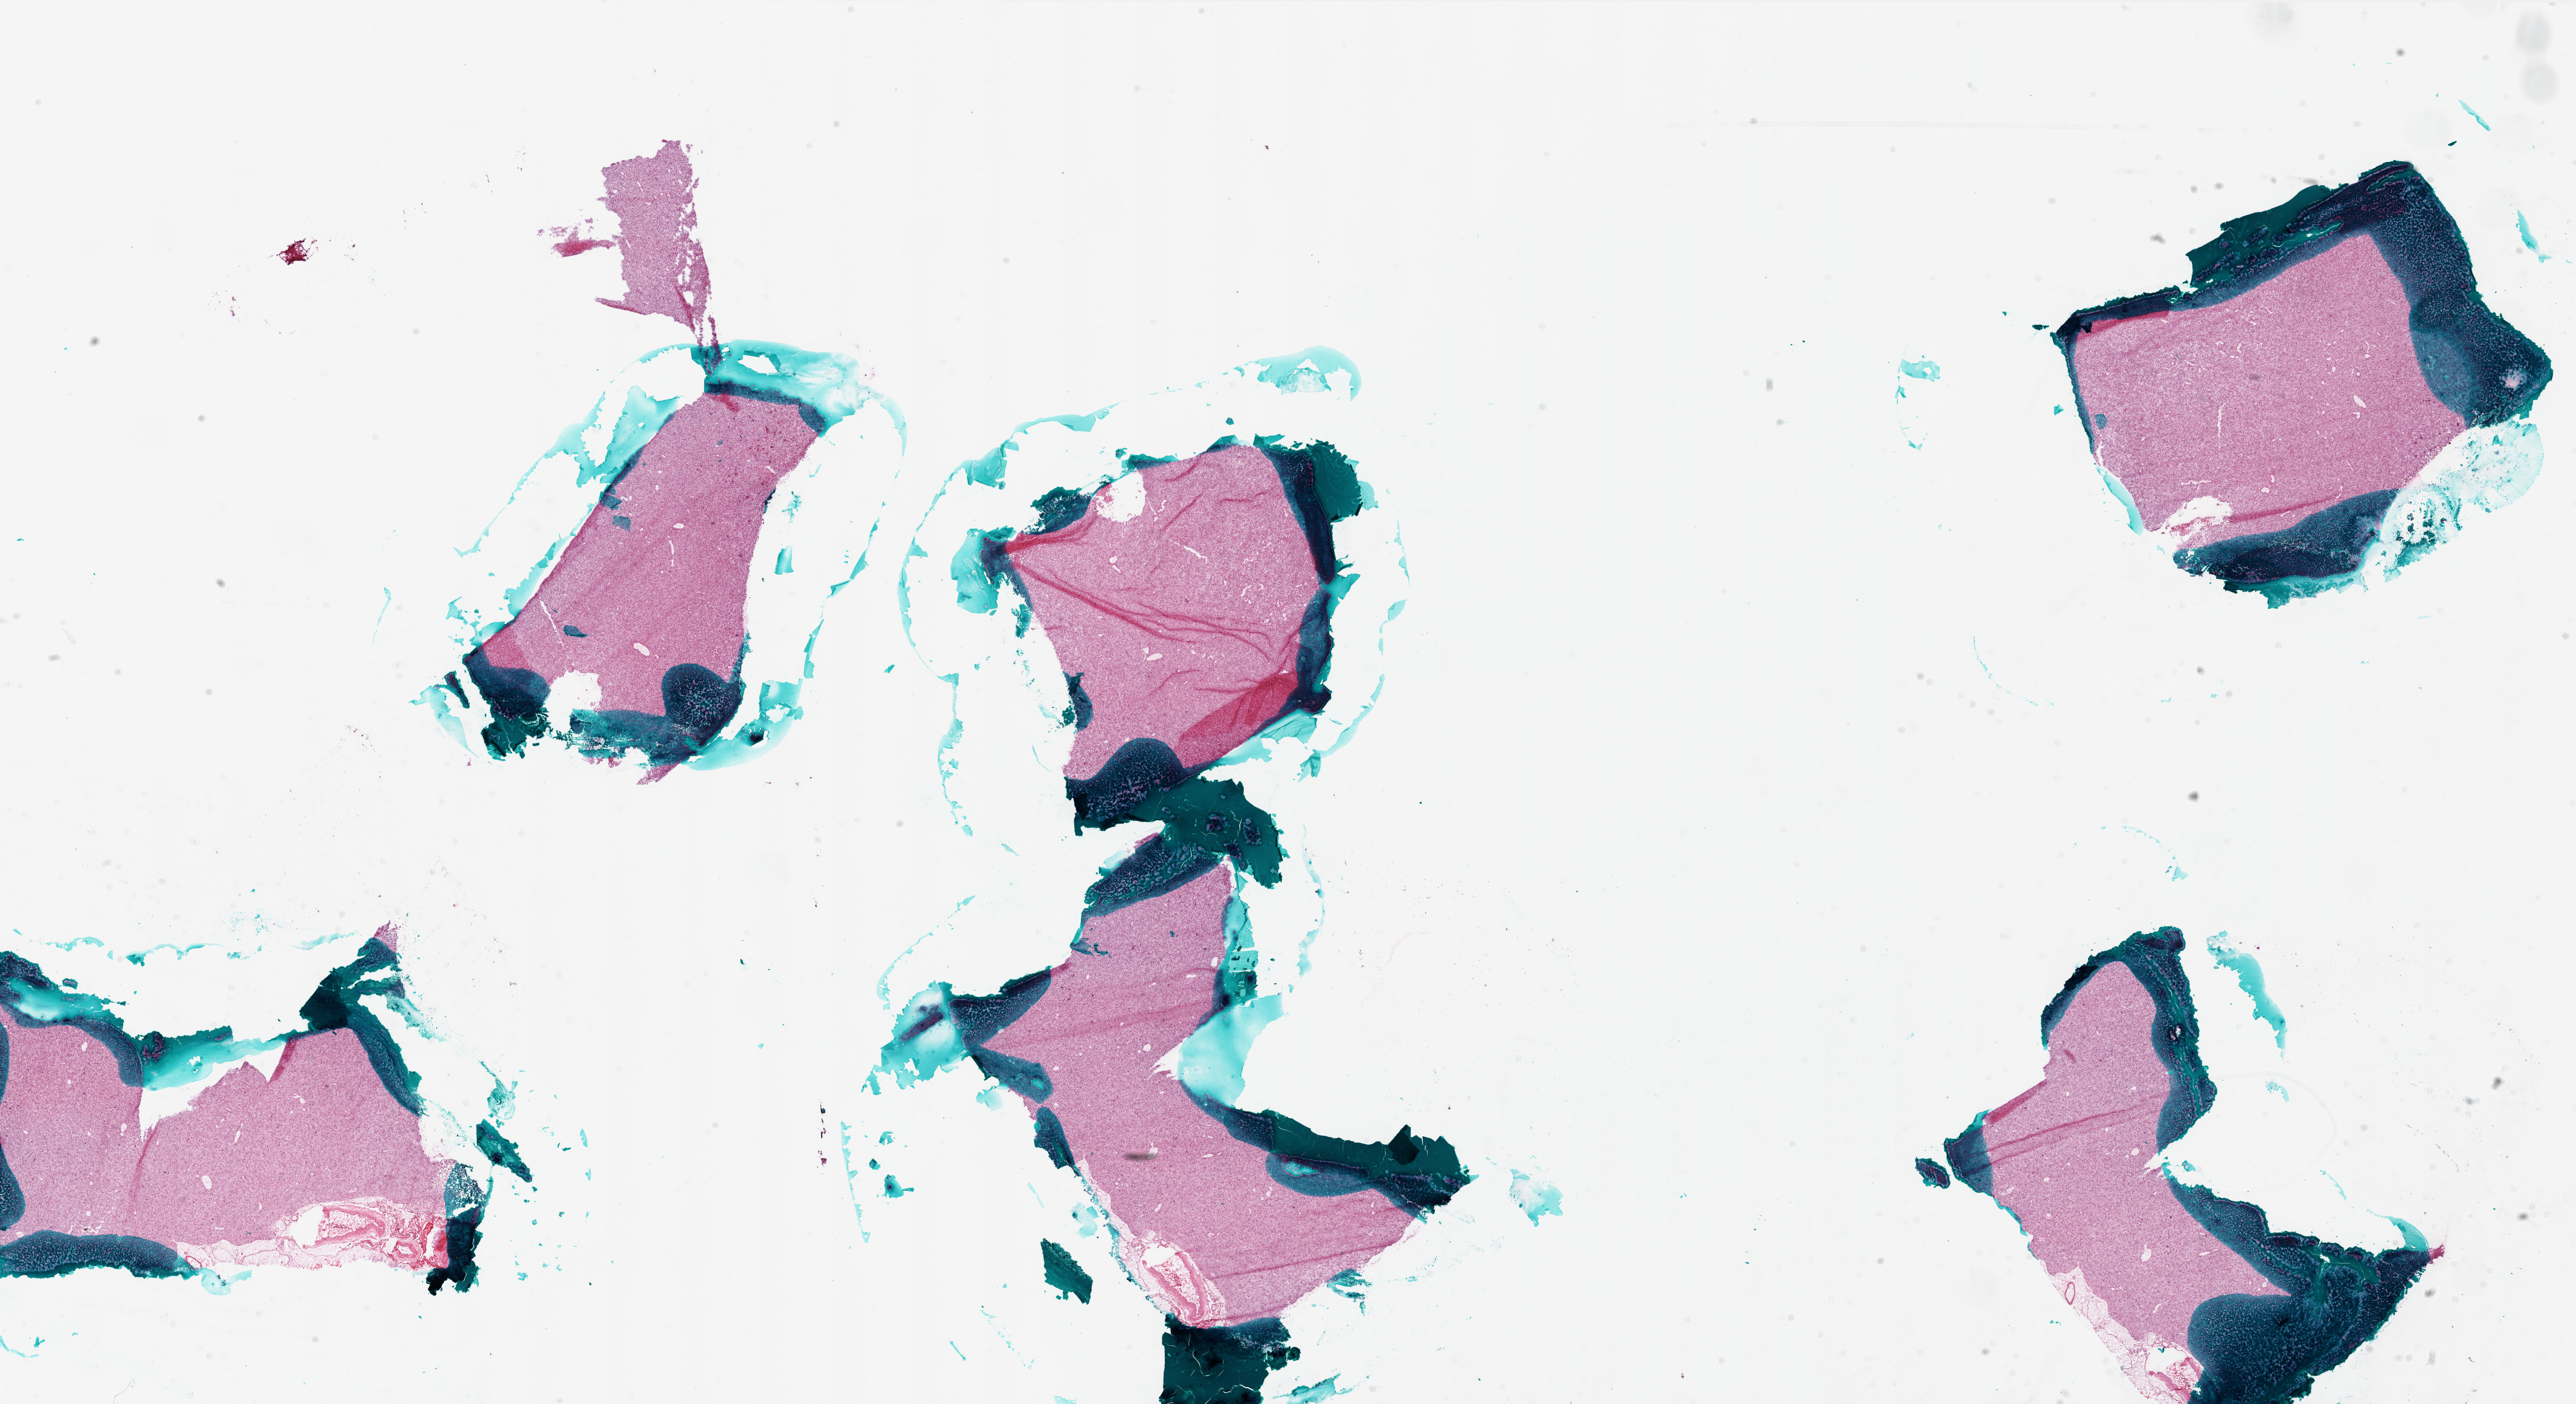
H&E-stained whole-slide image — shown as a low-resolution overview of the whole scanned area (about 34.0 x 18.5 mm, acquisition: 20x scan), frozen section, primary tumour sample from the brain. Male patient; age at initial diagnosis 50 years. Slide review estimates, as recorded: tumour cells 95%, tumour nuclei 85%, normal cells 0%, stromal cells 5%, necrosis 0%.
* diagnosis: Glioblastoma